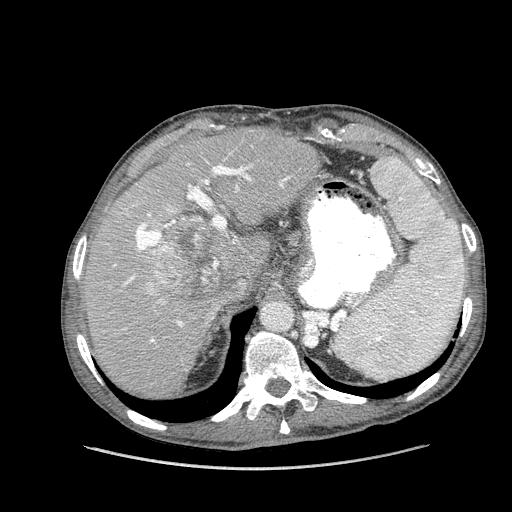
Contrast-enhanced abdominal CT (liver protocol), one axial slice. Slice 105 of 162 in the series (ordered by position). Soft-tissue window (W 400 / L 40 HU). 2.5 mm slice thickness. 512 × 512 image matrix. From the clinical record (not read from this slice): diagnosis: hepatocellular carcinoma (patient treated with transarterial chemoembolisation; whether this scan precedes or follows treatment is not stated here); TNM stage (as recorded): Stage-IIIA; Child-Pugh class: A; tumour nodularity: multinodular; tumour size: 9.9 cm.
Annotated regions visible in this slice (semi-automatic segmentation, software-assisted and operator-edited):
- liver parenchyma outside the tumour (the mass and vessels are separate outlines, so this box may not span the whole liver): bounding box [x1, y1, x2, y2] px = [83, 126, 320, 398]
- mass: [153, 213, 235, 301]
- liver vessels: [114, 159, 290, 342]